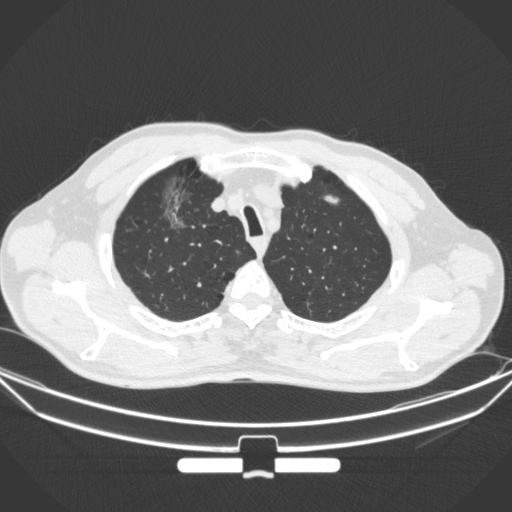
Chest CT, one axial slice; slice 290 of 355 in the series (ordered by position); 120 kVp; lung window (W 1500 / L -600 HU); 1 mm slice thickness; 512 × 512 image matrix. Patient: male, 67 years. From the clinical record (not read from this slice): clinical TNM (as recorded): T1c N0 M0; histopathological grade: G2.
Annotated regions visible in this slice (bounding box drawn by a radiologist):
- lung tumour (recorded histology: adenocarcinoma): bounding box <157,173,193,236> (left, top, right, bottom; pixels)